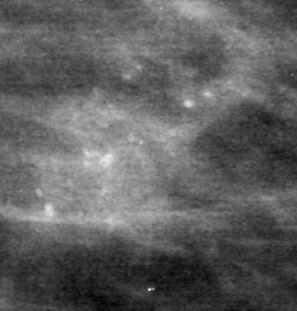
Region of interest cut from a scanned film mammogram (one marked finding), right breast, MLO view.
- Marked abnormality: calcifications, morphology pleomorphic, distribution linear; BI-RADS assessment category 4; pathology result (as recorded, not read from the image): malignant.